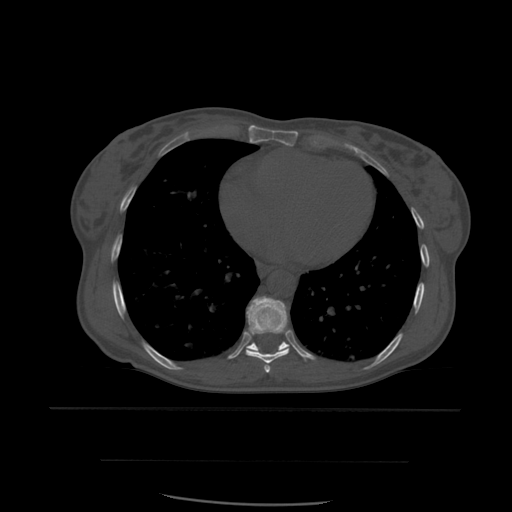
CT including the spine, one axial slice; position 350 of 574 along the scan axis; bone window (W 1800 / L 400 HU); 1.25 mm slice thickness; 512 × 512 image matrix, field of view 392 × 392 mm. Patient age 48 years. From the clinical record (not read from this slice): primary cancer: lung.
Annotated regions visible in this slice (semi-automatically segmented with operator editing):
- T7 vertebra: bounding box <265,367,270,373> (left, top, right, bottom; pixels)
- T8 vertebra: <246,297,289,373>
- T9 vertebra: <238,337,316,361>